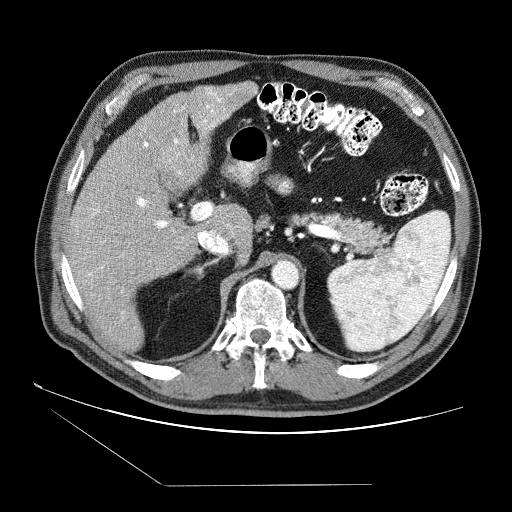
Contrast-enhanced abdominal CT (liver protocol), one axial slice. Position 48 of 87 along the scan axis. Soft-tissue window (W 400 / L 40 HU). 512 × 512 image matrix. From the clinical record (not read from this slice): diagnosis: hepatocellular carcinoma (patient treated with transarterial chemoembolisation; whether this scan precedes or follows treatment is not stated here); TNM stage (as recorded): Stage-II; Child-Pugh class: B.
Annotated regions visible in this slice (semi-automatically segmented with operator editing):
- liver parenchyma outside the tumour (the mass and vessels are separate outlines, so this box may not span the whole liver): bounding box (x1, y1, x2, y2) in pixels: (66, 82, 256, 350)
- mass: (72, 220, 80, 233)
- liver vessels: (88, 88, 231, 314)